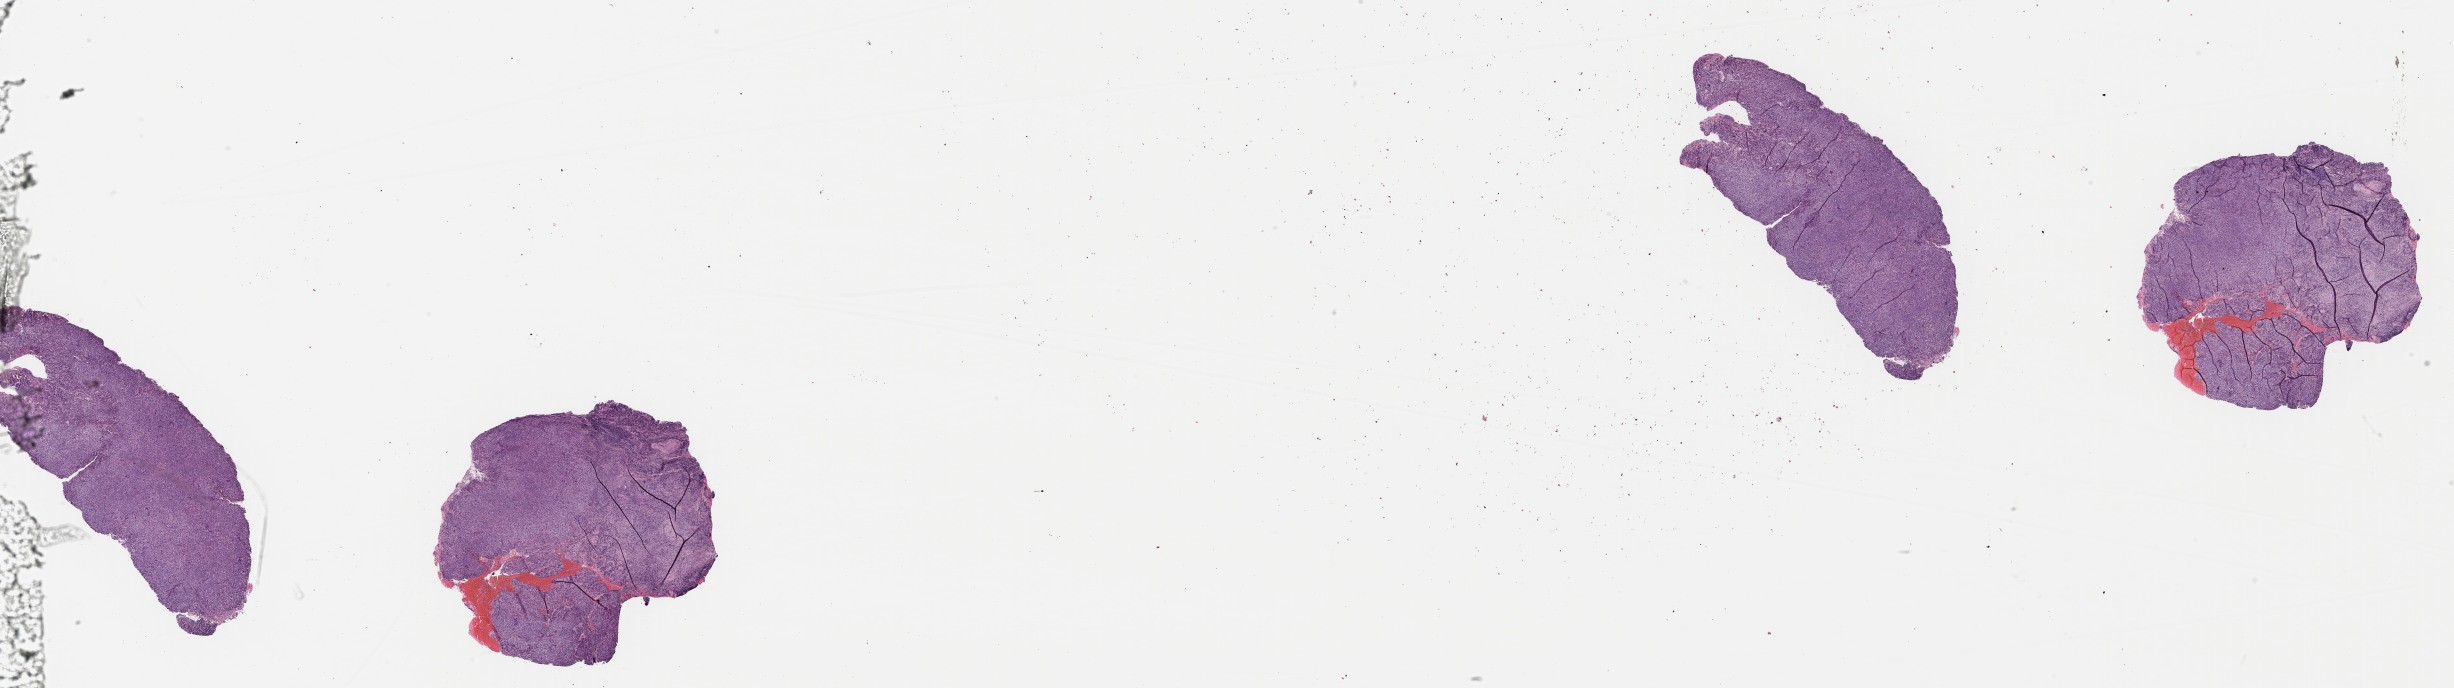
Digitized Hematoxylin and eosin (H&E) stained tissue section (whole slide) — shown as a low-resolution overview of the whole scanned area (about 38.7 x 10.9 mm, from a 40x scan); formalin-fixed paraffin-embedded (FFPE) diagnostic section; primary tumour sample from the cervix. Female patient; age at initial diagnosis 35 years. Histologic grade: G3 (poorly differentiated).
• histologic diagnosis: Squamous cell carcinoma, NOS
• FIGO stage: IIA